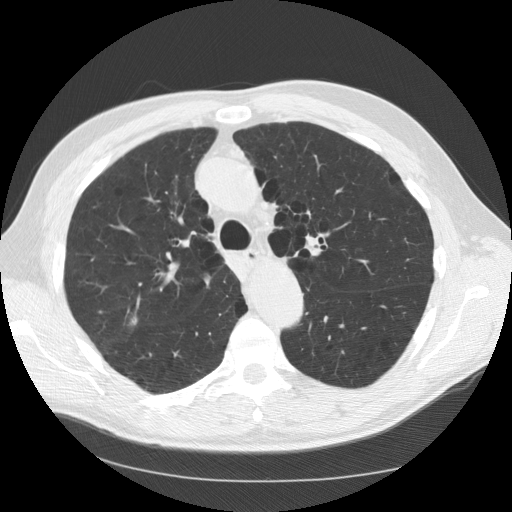
Low-dose screening chest CT, one axial slice. Slice 89 of 133 in the series (ordered by position). Lung window (W 1500 / L -600 HU). 2.5 mm slice thickness. 512 × 512 image matrix.
Structures marked on this image (outlined manually by an expert reader):
- lesion 1 (tumor, upper lobe of right lung): bounding box <130,316,137,325> (left, top, right, bottom; pixels)